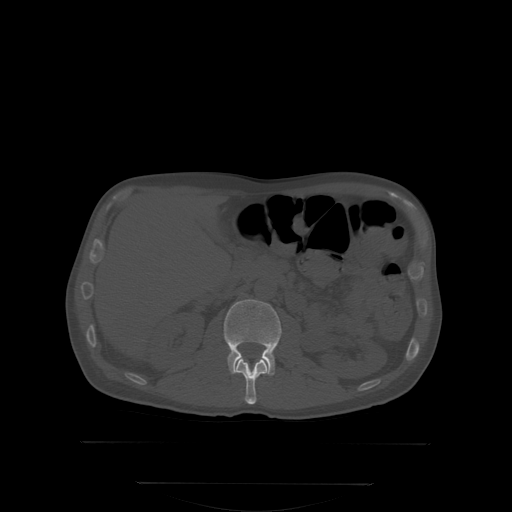
CT including the spine, one axial slice; slice 144 of 350 in the series (ordered by position); bone window (W 1800 / L 400 HU); 512 × 512 image matrix, field of view 500 × 500 mm. Male patient, age 58 years. From the clinical record (not read from this slice): primary cancer: prostate.
Structures marked on this image (semi-automatic segmentation, software-assisted and operator-edited):
- L1 vertebra: bounding box (x1, y1, x2, y2) in pixels: (235, 357, 269, 404)
- L2 vertebra: (223, 299, 282, 373)